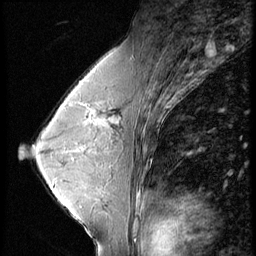
Breast MRI (dynamic contrast-enhanced), one sagittal slice; position 38 of 56 along the scan axis; 4 images stored at this slice position (order not interpretable as contrast timing); 1.5 T; TE 4.2 ms, TR 9 ms; 2.5 mm slice thickness; 256 × 256 image matrix, field of view 180 × 180 mm. Patient: female, 45 years. From the clinical record (not read from this slice): setting: breast cancer imaged before/during neoadjuvant chemotherapy; receptor status: triple-negative.
Structures marked on this image (semi-automatic segmentation, software-assisted and operator-edited):
- analysis volume of interest (the breast-tissue region the enhancement analysis was run in; not a lesion): bounding box (x1, y1, x2, y2) in pixels: (77, 104, 97, 124)
- tumour enhancement mask (voxels above the 140 % enhancement threshold inside the analysis volume of interest): (77, 104, 97, 124)